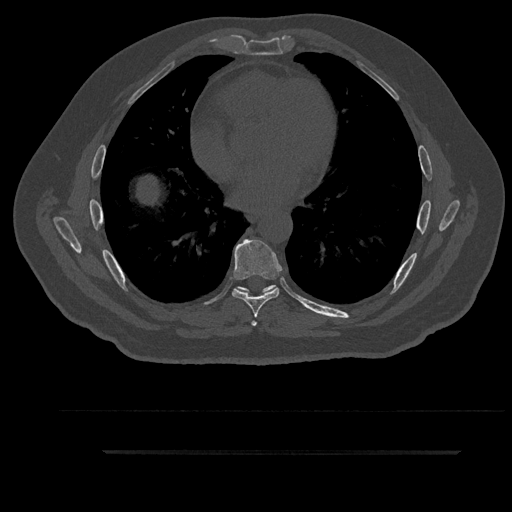
CT including the spine, one axial slice. Slice 516 of 797 in the series (ordered by position). Reconstruction kernel Br40s/3. 120 kVp. Bone window (W 1800 / L 400 HU). 0.5 mm slice thickness. 512 × 512 image matrix. Male patient, age 63 years. Case-level facts recorded for this patient, not image findings: primary cancer: renal.
Structures marked on this image (semi-automatically segmented with operator editing):
- T6 vertebra: box from (x=235, y=285) to (x=275, y=326) px
- T7 vertebra: (x=232, y=239)–(x=283, y=318)
- T8 vertebra: (x=242, y=285)–(x=277, y=291)